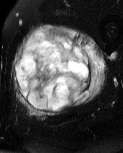
MRI of an extremity soft-tissue mass, one axial slice. Slice 22 of 60 in the series (ordered by position). T2-weighted fat-saturated. MR volume resampled by the dataset authors to the PET/CT grid (not the native acquisition matrix). 3.27 mm slice thickness. 123 × 153 image matrix, field of view 120 × 149 mm. Male patient. Case-level facts recorded for this patient, not image findings: histological type: pleiomorphic liposarcoma; grade: high; site of the primary tumour: left thigh.
Annotated regions visible in this slice (expert contour drawn on MRI and transferred to this co-registered scan by the dataset authors):
- gross tumour volume including surrounding oedema: box from (x=13, y=24) to (x=108, y=117) px
- gross tumour volume (mass): (x=17, y=31)–(x=92, y=112)